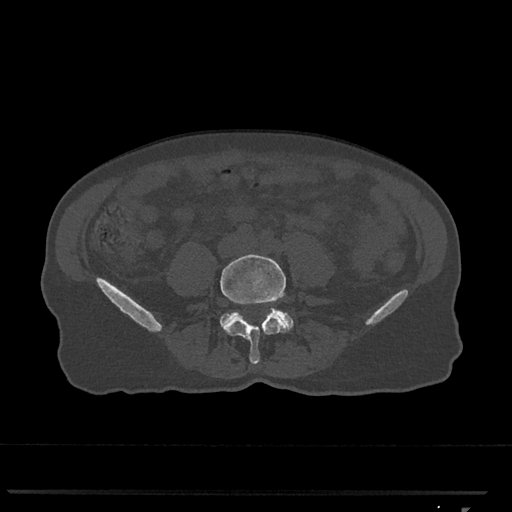
CT including the spine, one axial slice; position 190 of 793 along the scan axis; 120 kVp; bone window (W 1800 / L 400 HU); 0.5 mm slice thickness; 512 × 512 image matrix. Patient: female, 62 years. From the clinical record (not read from this slice): primary cancer: renal.
Outlined on this slice (semi-automatically segmented with operator editing):
- L4 vertebra: box from (x=220, y=254) to (x=289, y=364) px
- L5 vertebra: (x=220, y=308)–(x=294, y=330)